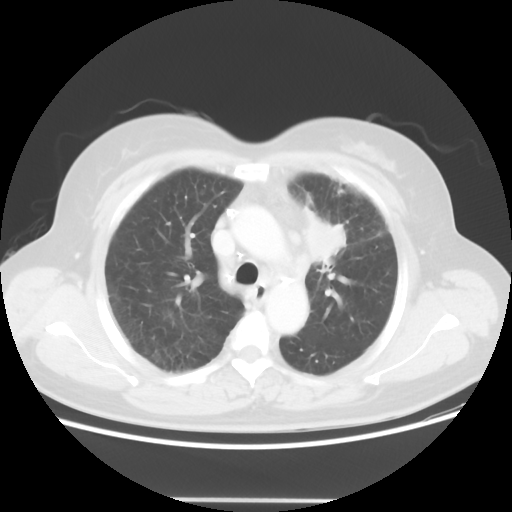
Chest CT, one axial slice. Position 39 of 52 along the scan axis. 120 kVp. Lung window (W 1500 / L -600 HU). 512 × 512 image matrix. Patient: female, 52 years. From the clinical record (not read from this slice): clinical TNM (as recorded): T2 N3 M0.
Annotated regions visible in this slice (rectangle marked by the reading radiologist):
- lung tumour (recorded histology: adenocarcinoma): box from (x=294, y=192) to (x=352, y=270) px